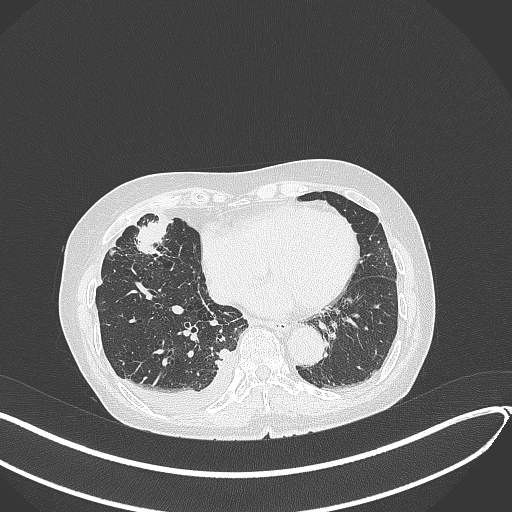
Chest CT, one axial slice. Slice 130 of 418 in the series (ordered by position). 120 kVp. Lung window (W 1500 / L -600 HU). 1 mm slice thickness. 512 × 512 image matrix. Female patient, age 75 years. From the clinical record (not read from this slice): clinical TNM (as recorded): T2a N3 M0.
Annotated regions visible in this slice (rectangle marked by the reading radiologist):
- lung tumour (recorded histology: adenocarcinoma): bounding box (x1, y1, x2, y2) in pixels: (134, 216, 169, 261)